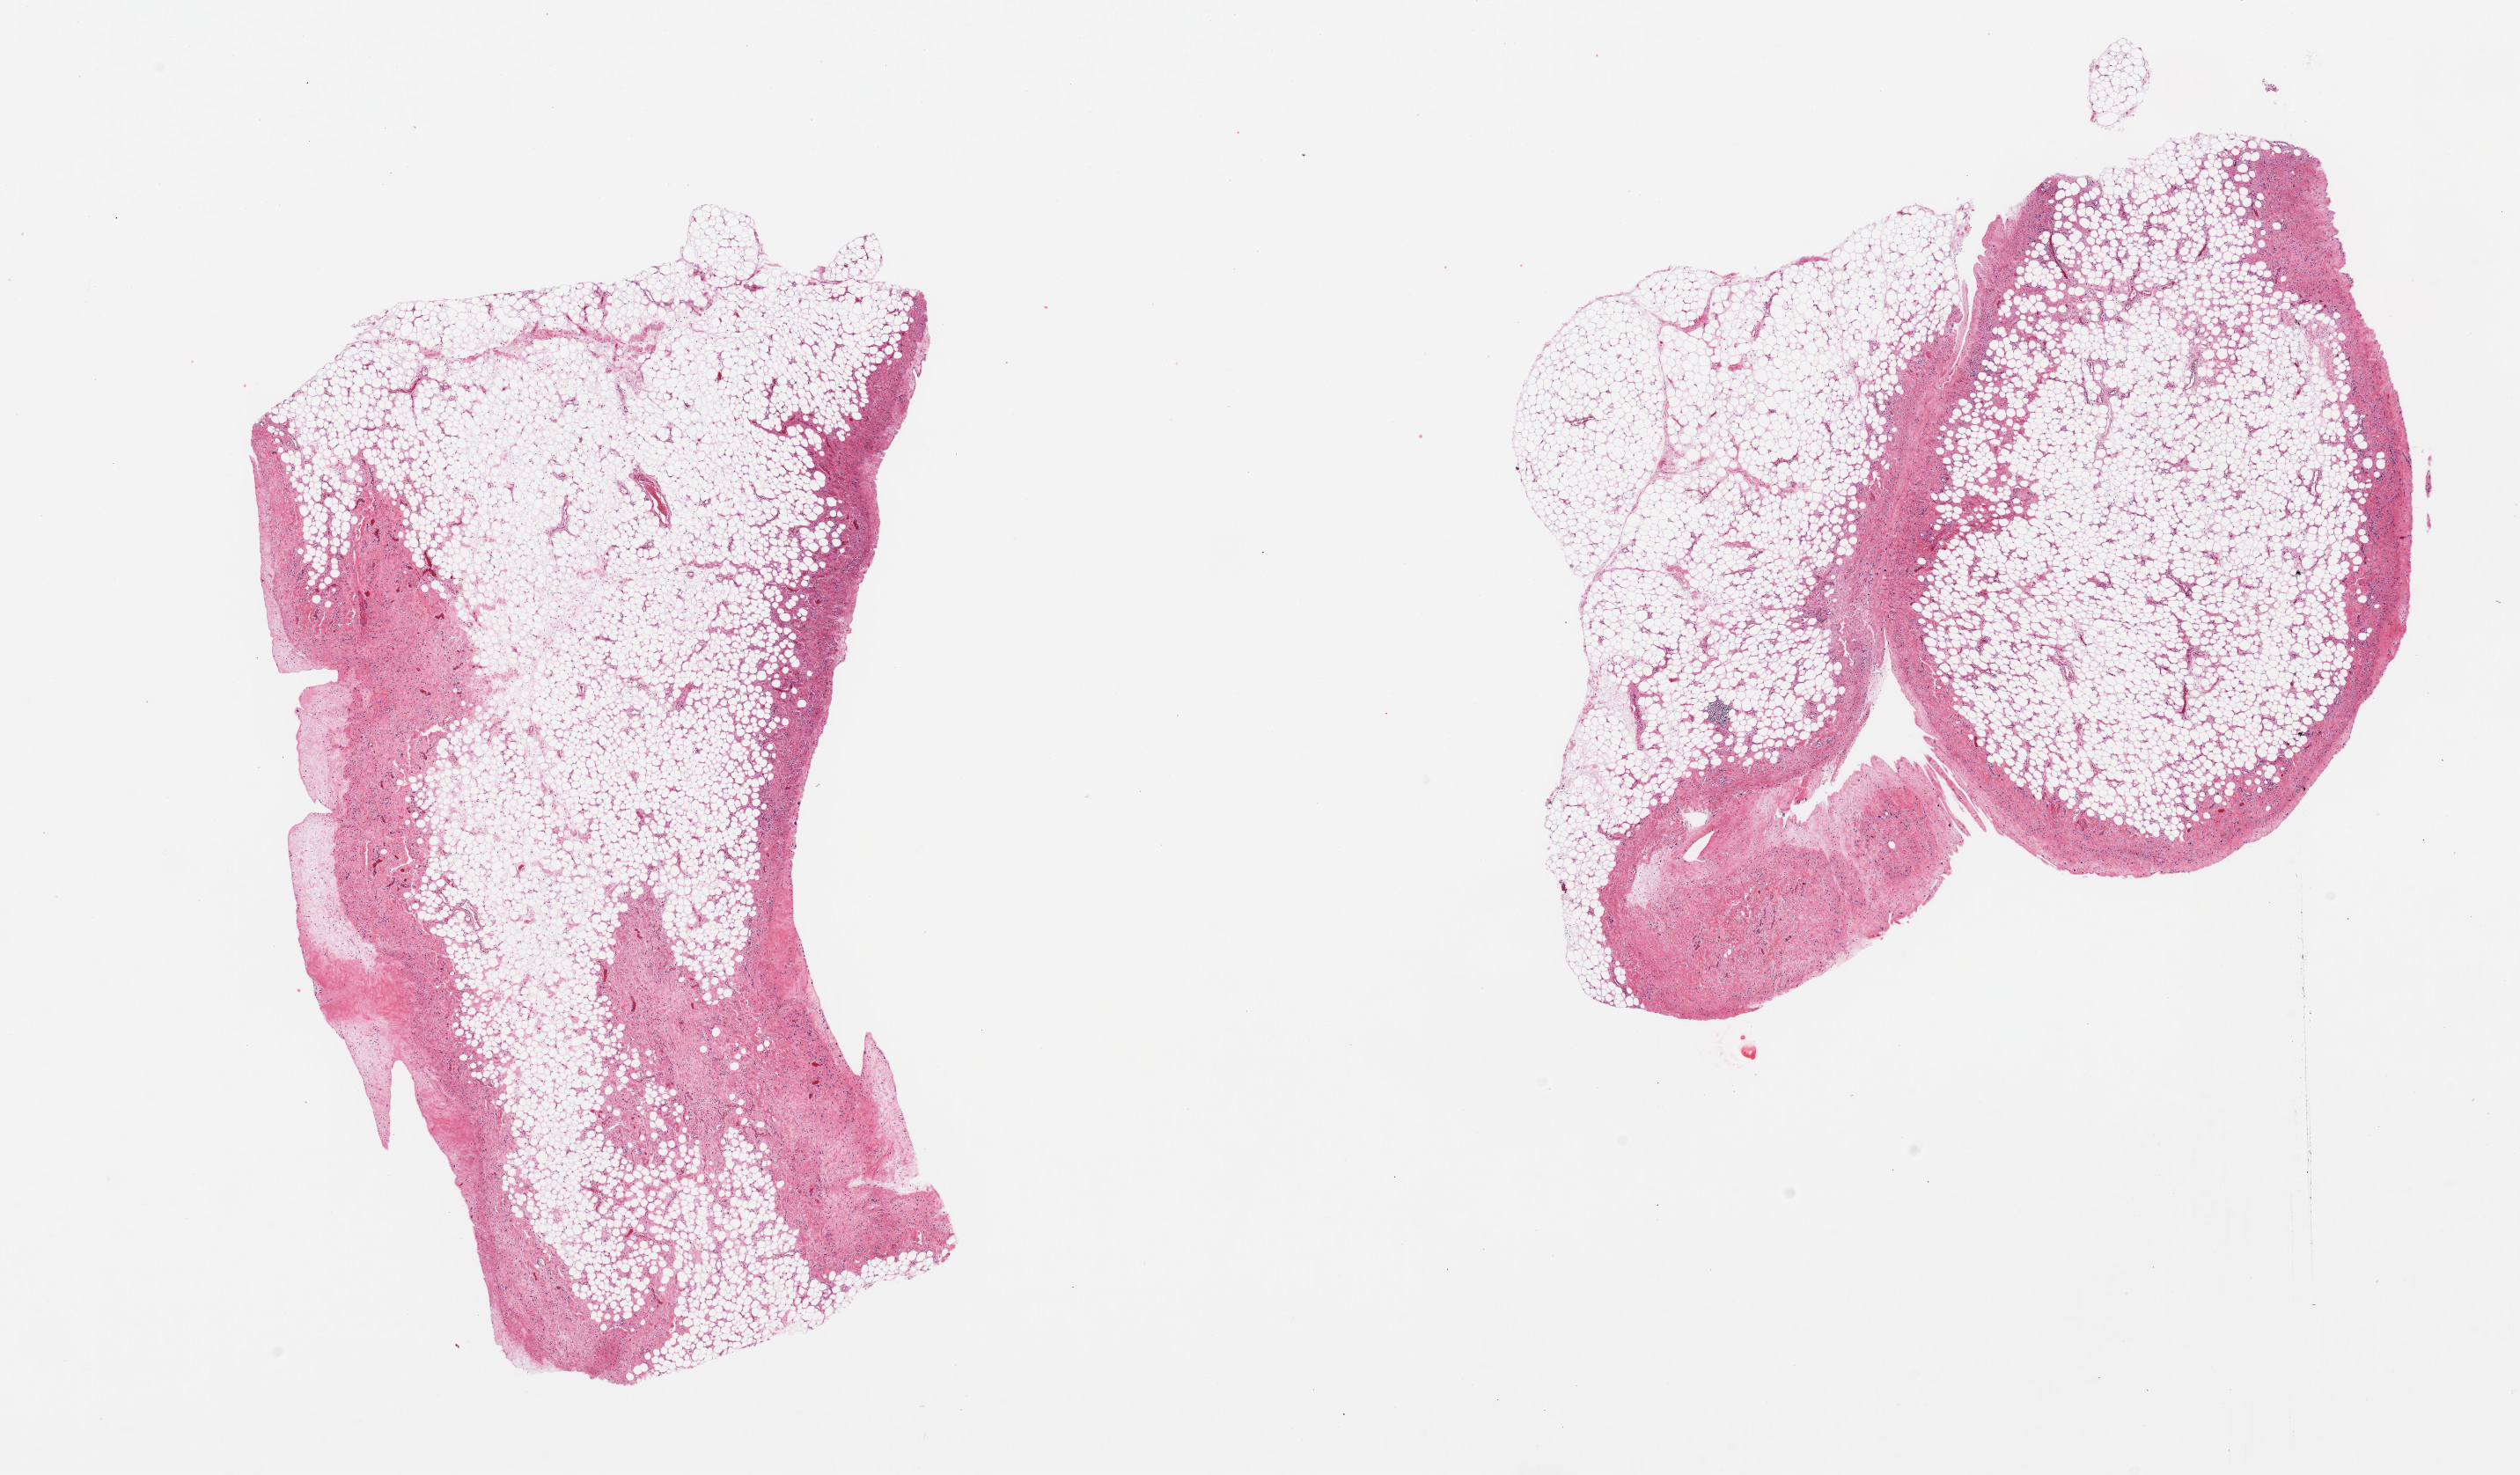
Whole-slide image, hematoxylin and eosin (H&E) stain, a low-resolution overview of the entire scanned area, about 22.6 x 13.3 mm. PAXgene-fixed, paraffin-embedded tissue. Section of omentum (target tissue). Tissue donor sample. Male donor.
Review note (as recorded): 2 pieces, exhuberent meosthelial hyperplastic fibrosis, ~30-40% of tissue.